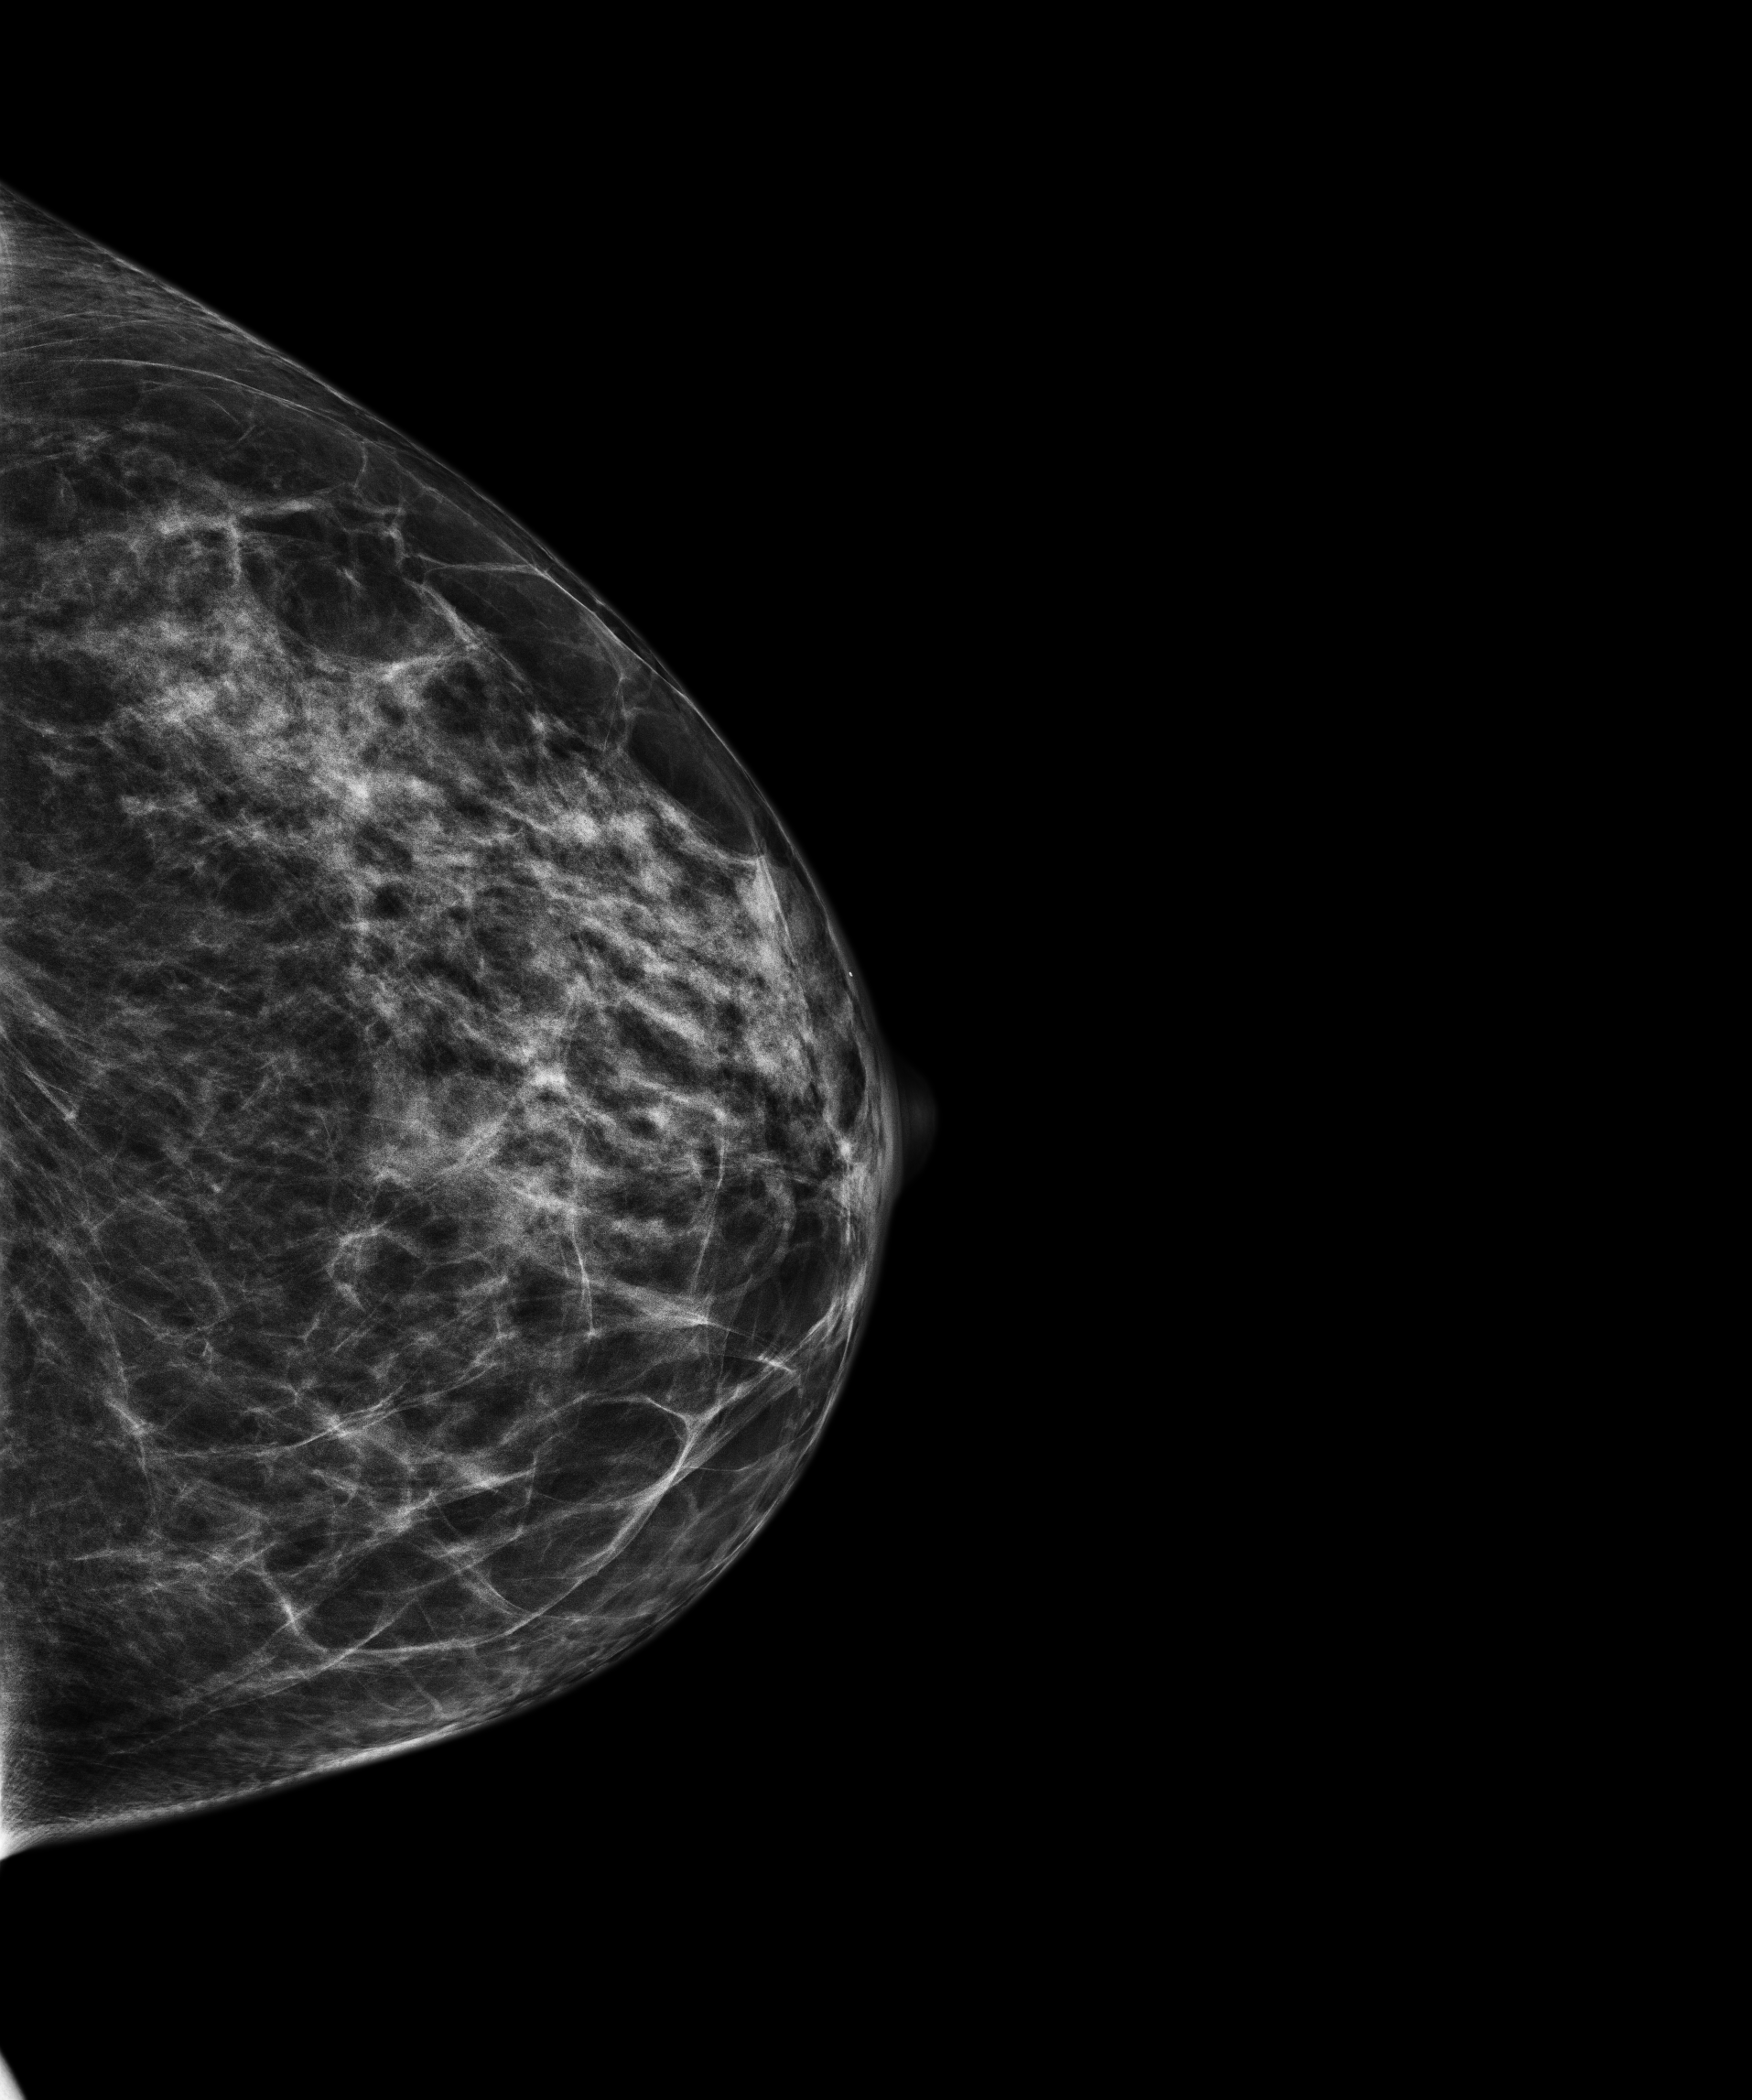
Annual screening mammography examination, compressed breast thickness 60 mm, system: Senographe Pristina. Female patient, age 57 years.
Image type: full-field digital mammogram. Breast: left. Projection: CC view.